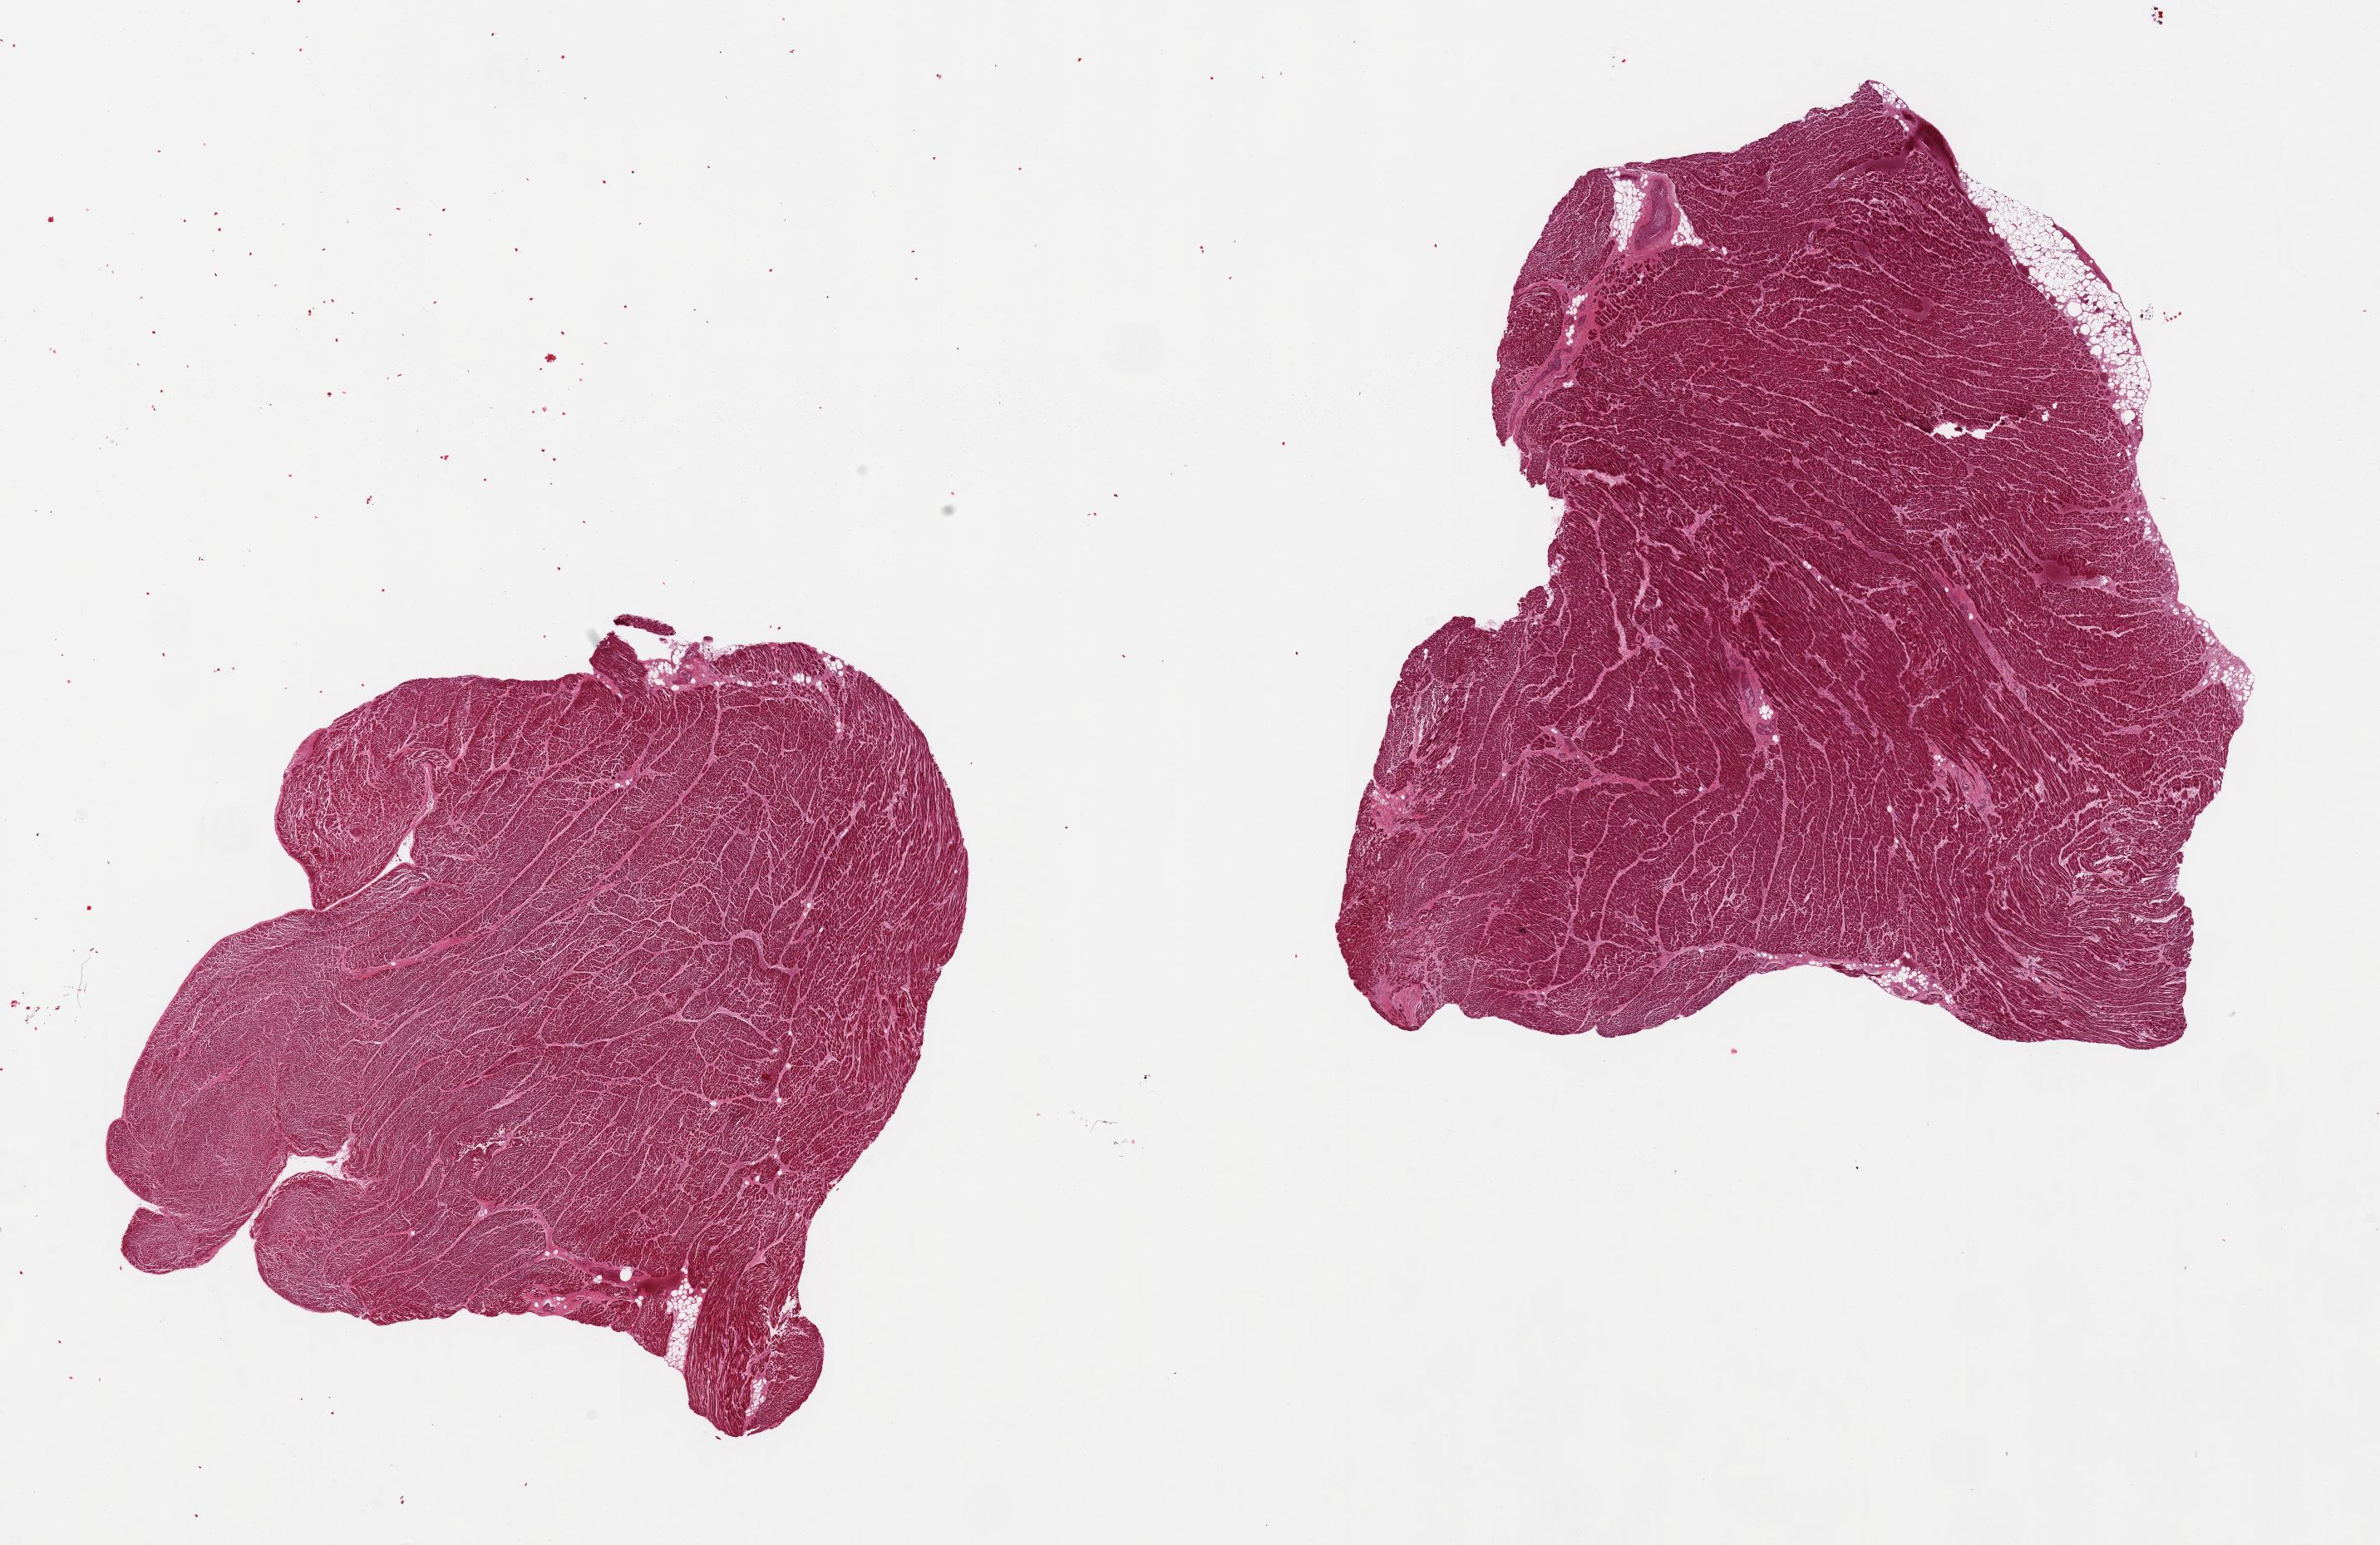
Digitized H&E-stained section, low-resolution overview of the scanned area, about 22.6 x 14.7 mm (acquisition: 20x scan), PAXgene-fixed, paraffin-embedded tissue, sampled site (target tissue): heart, donor tissue sample. Donor sex: male.
* review note (as recorded): 2 pieces moderate chronic ischemic changes, interstitial fibrosis, microinfarcts (remote)